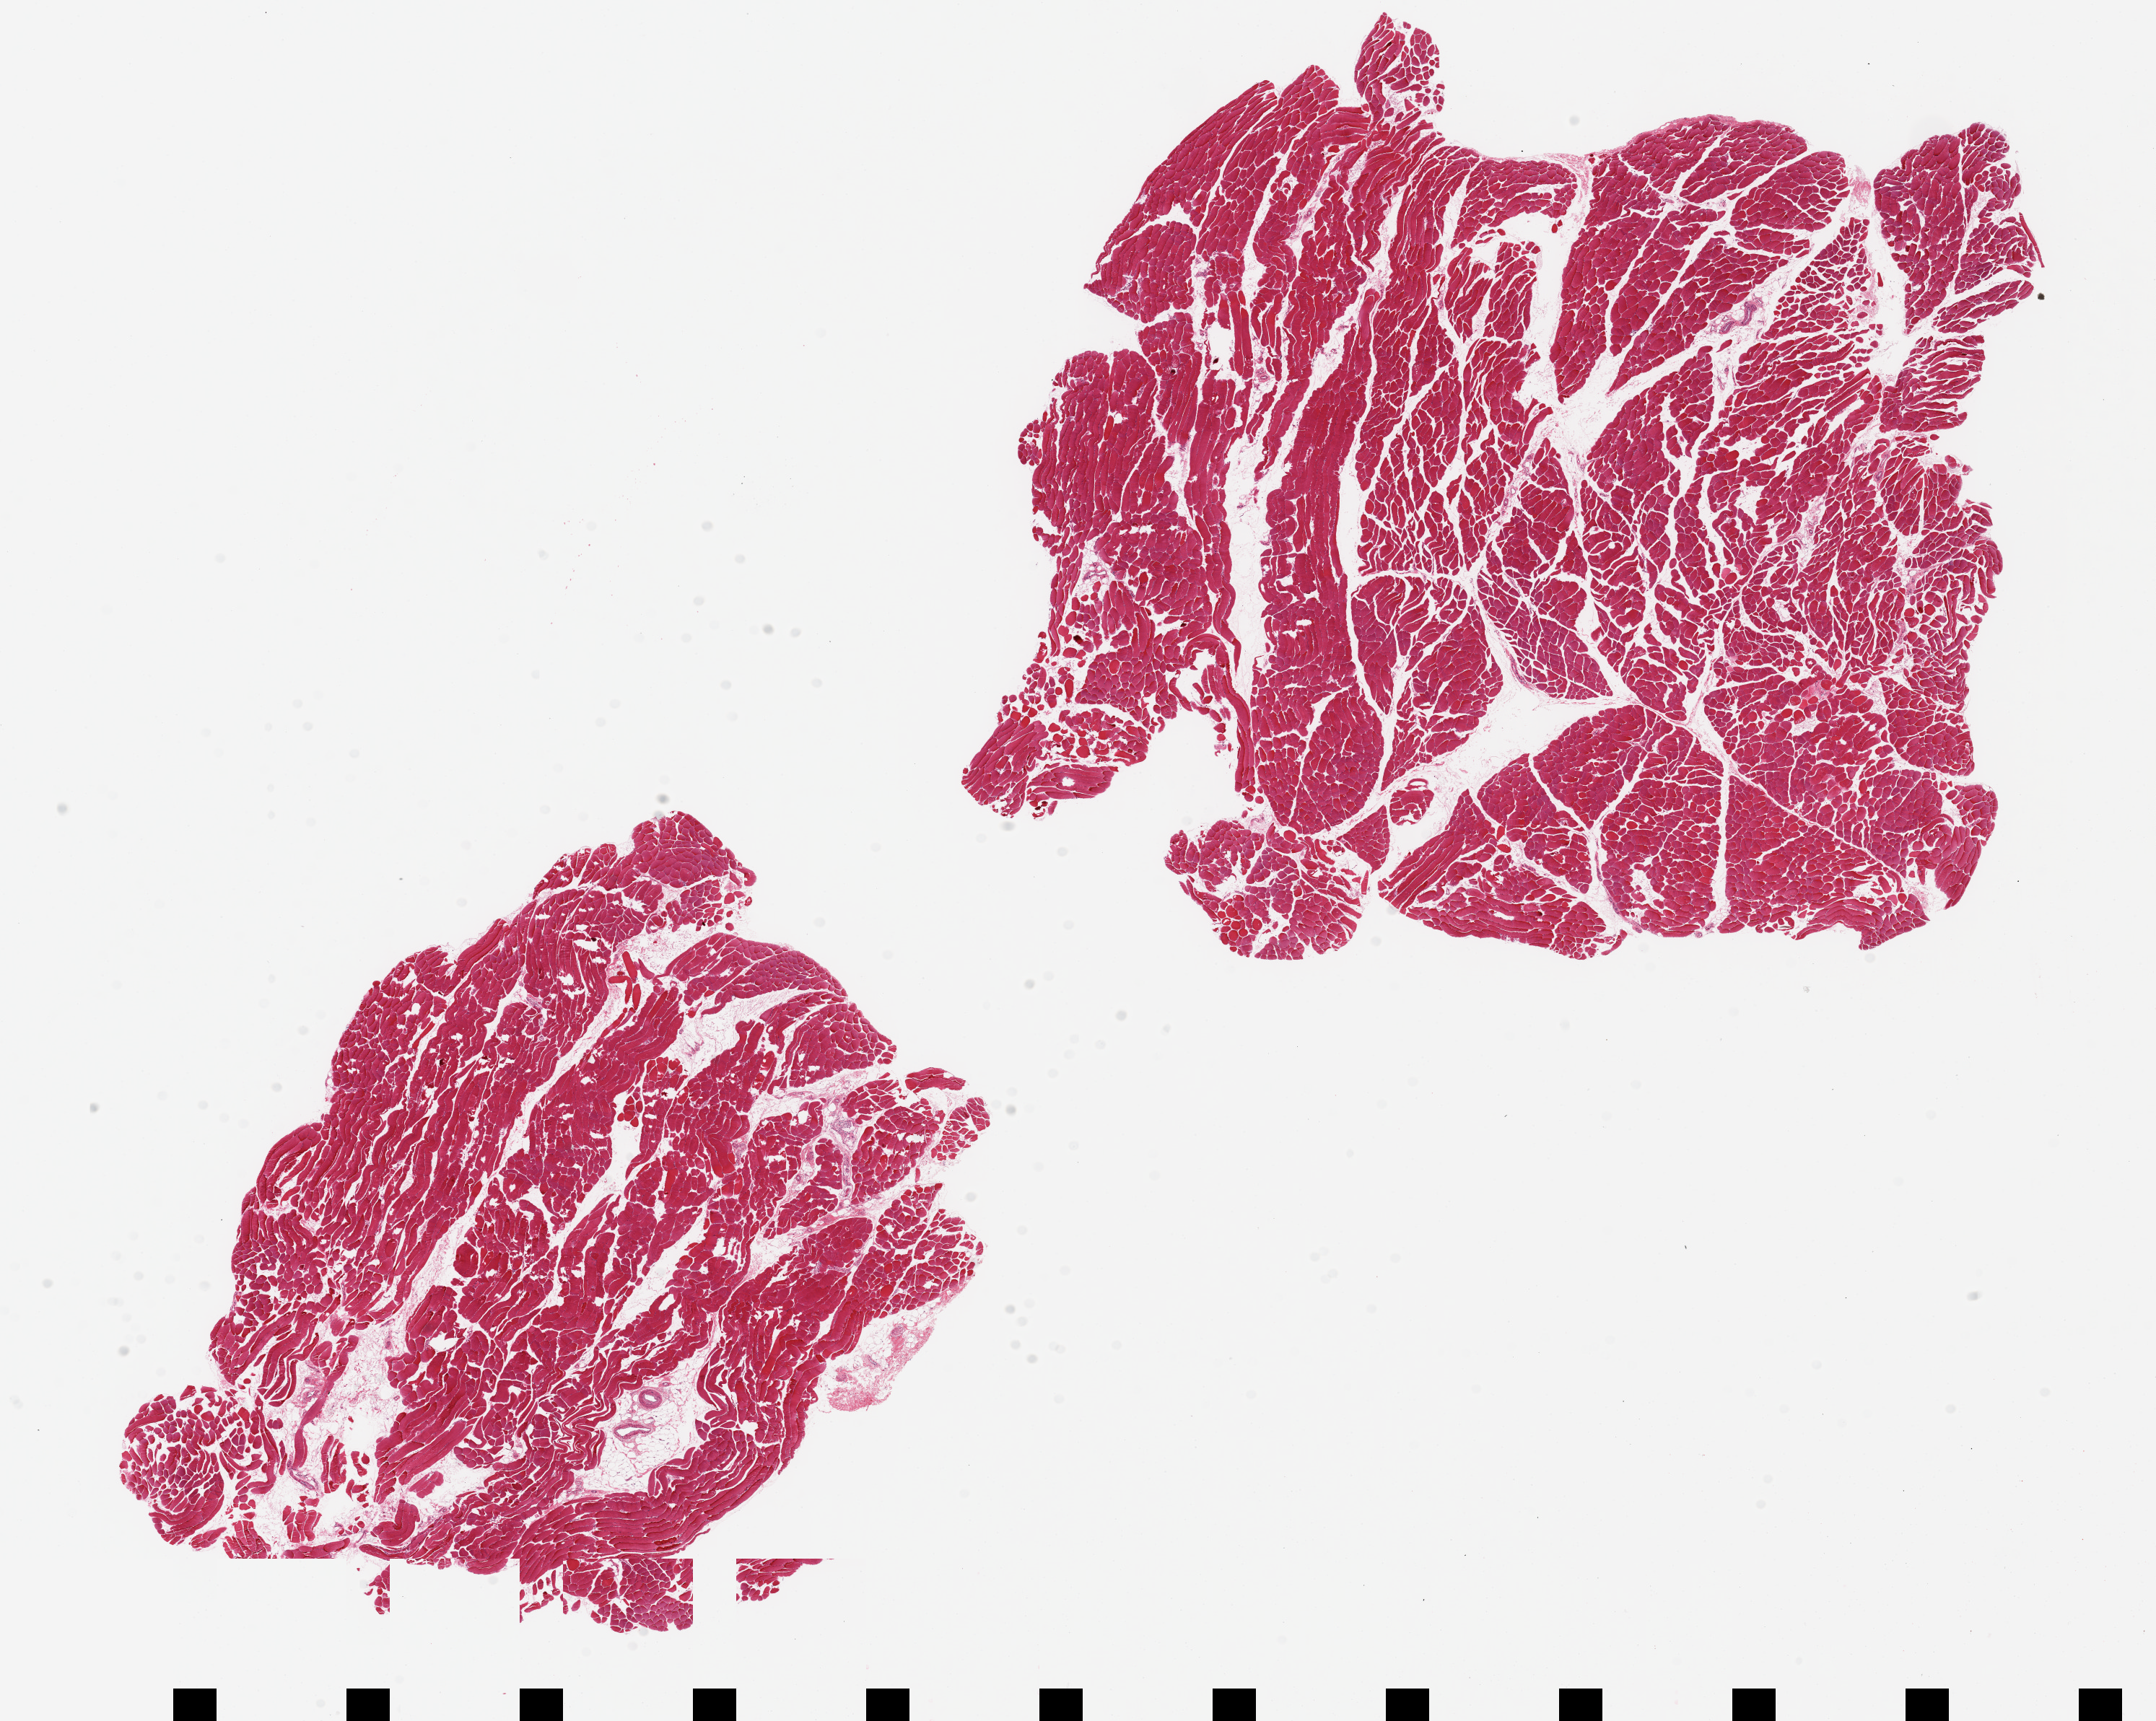
Whole-slide image, hematoxylin and eosin (H&E) stain, shown as a low-resolution overview of the whole scanned area (about 23.6 x 18.9 mm, slide scanned at 20x); PAXgene-fixed, paraffin-embedded tissue; section of skeletal muscle (target tissue); donor tissue sample. Male donor.
• review note (as recorded): 2 pieces ~10x8mm, minimal interstitial fat